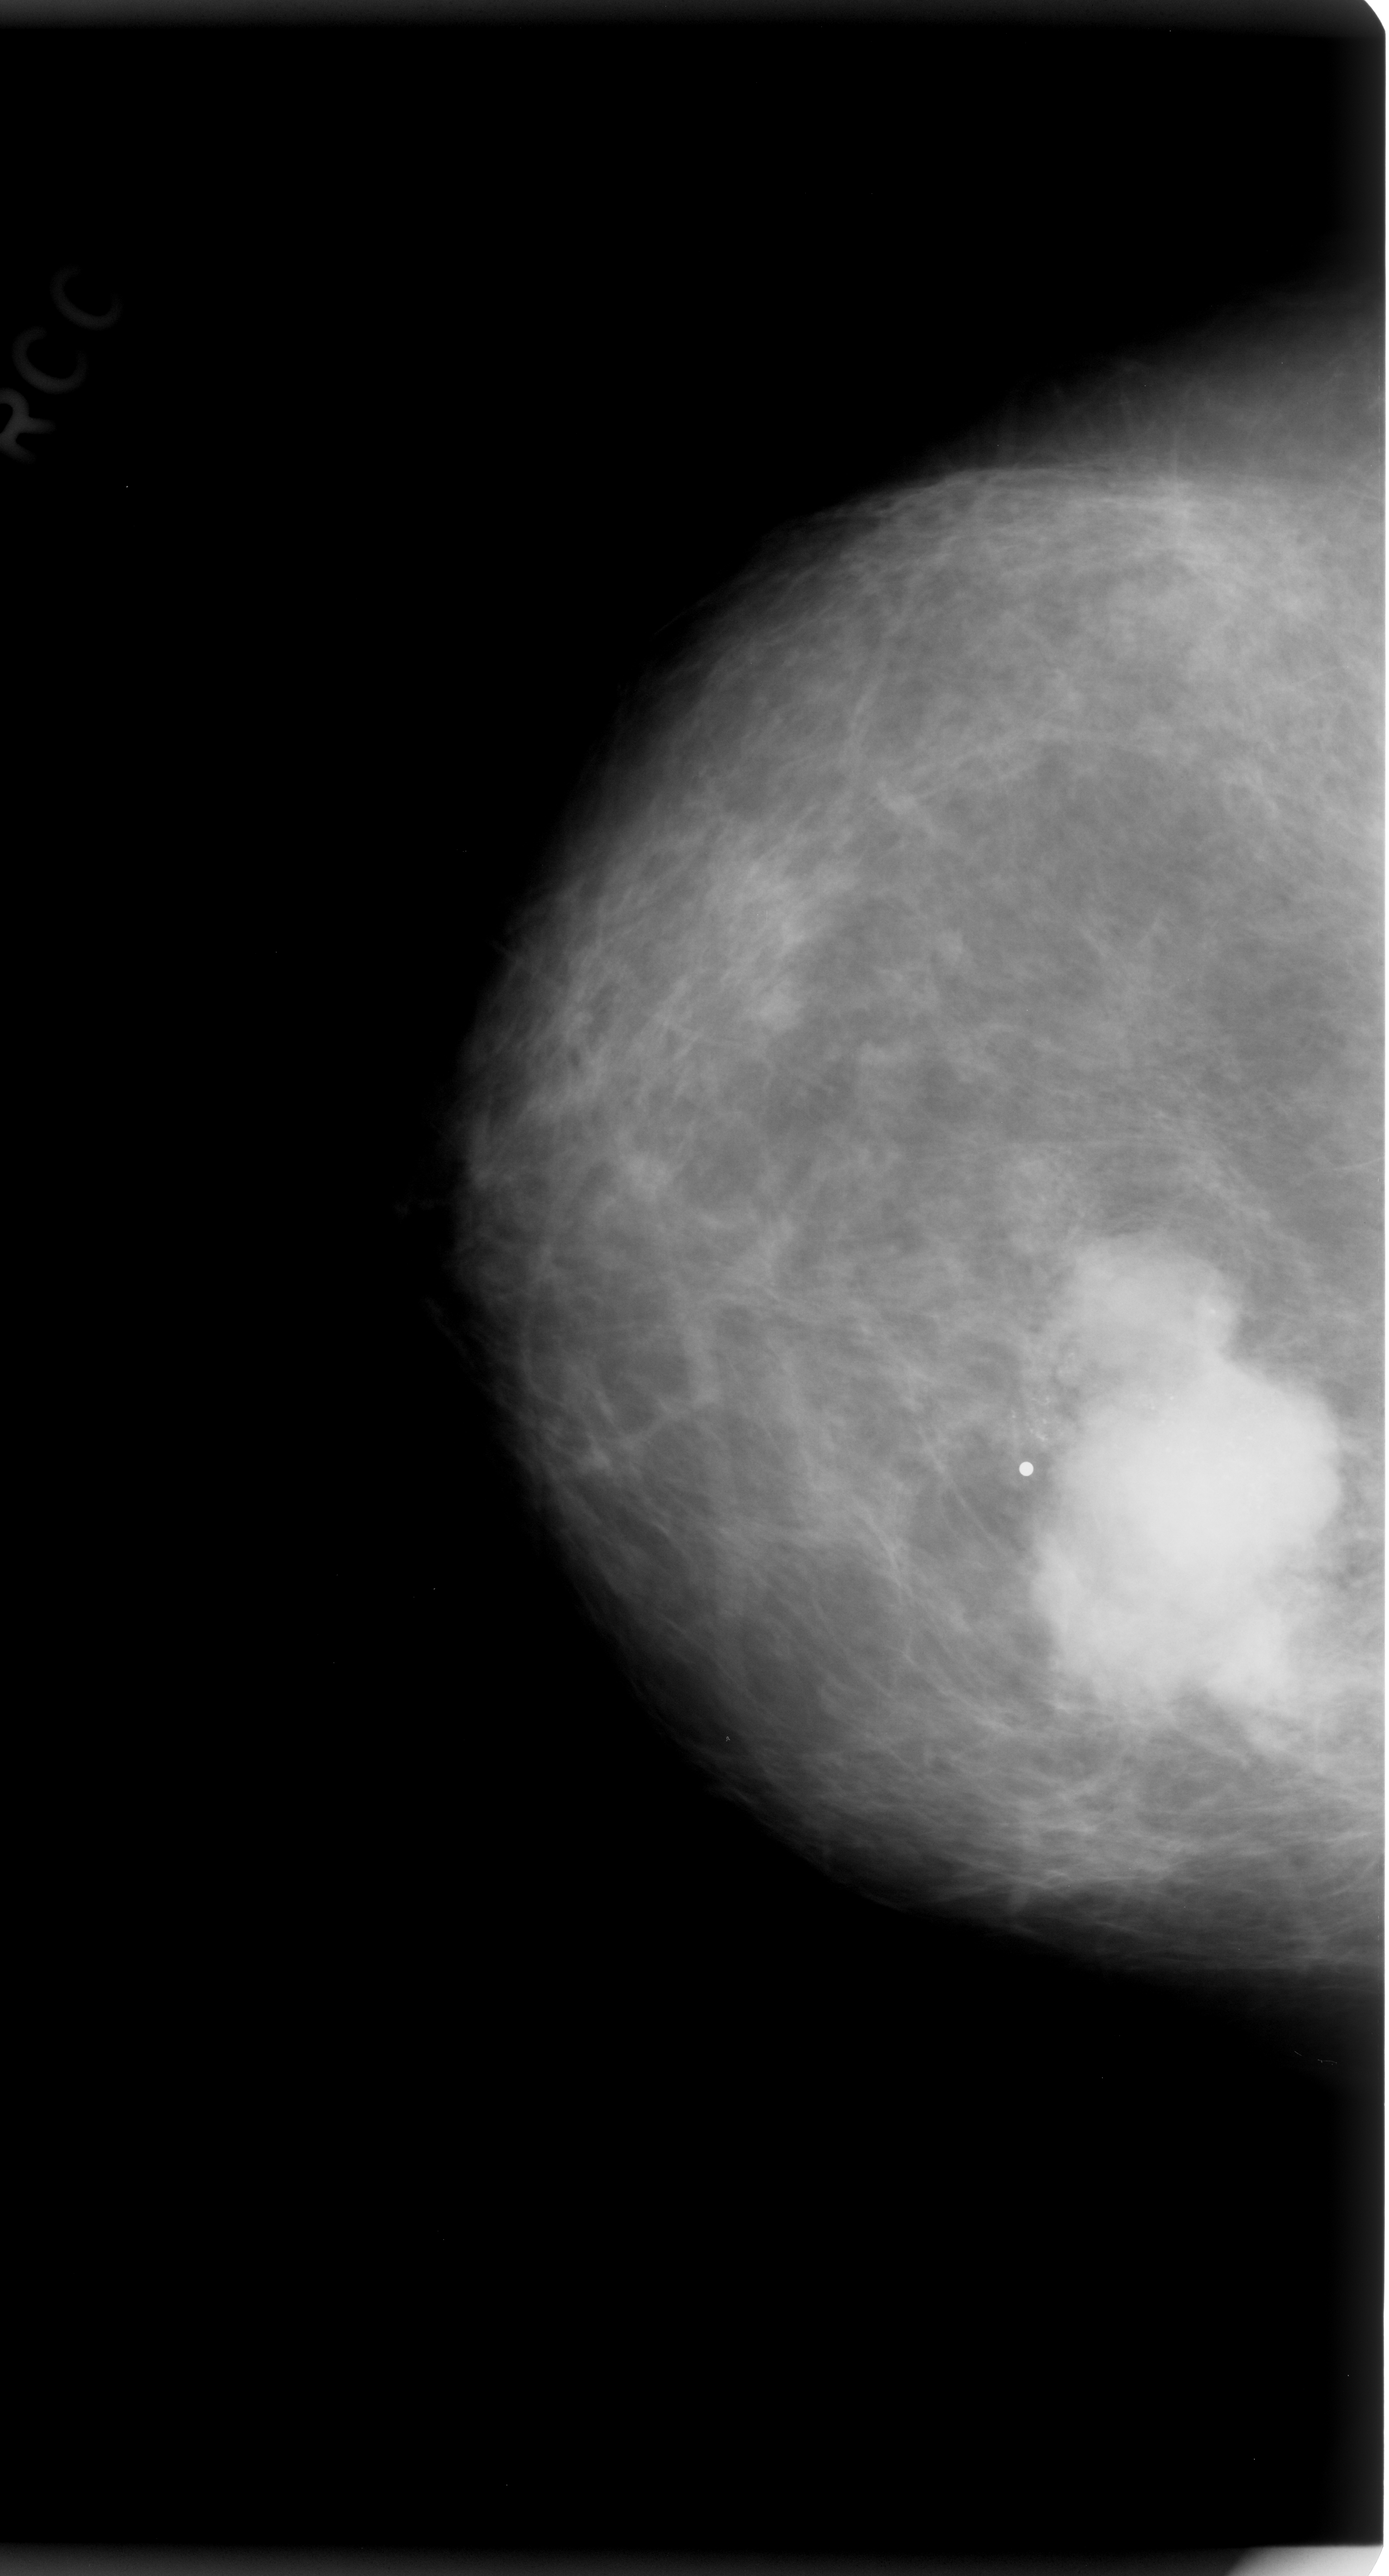
Scanned film-screen mammogram; right breast; craniocaudal (CC) view; BI-RADS breast density category 1 (scale 1–4); 1389 × 2576 image matrix.
Expert-marked regions of interest on this film, with their recorded descriptors:
- calcifications, morphology pleomorphic, distribution clustered; BI-RADS assessment category 5; pathology (as recorded): malignant: box from (x=910, y=1099) to (x=1386, y=1896) px